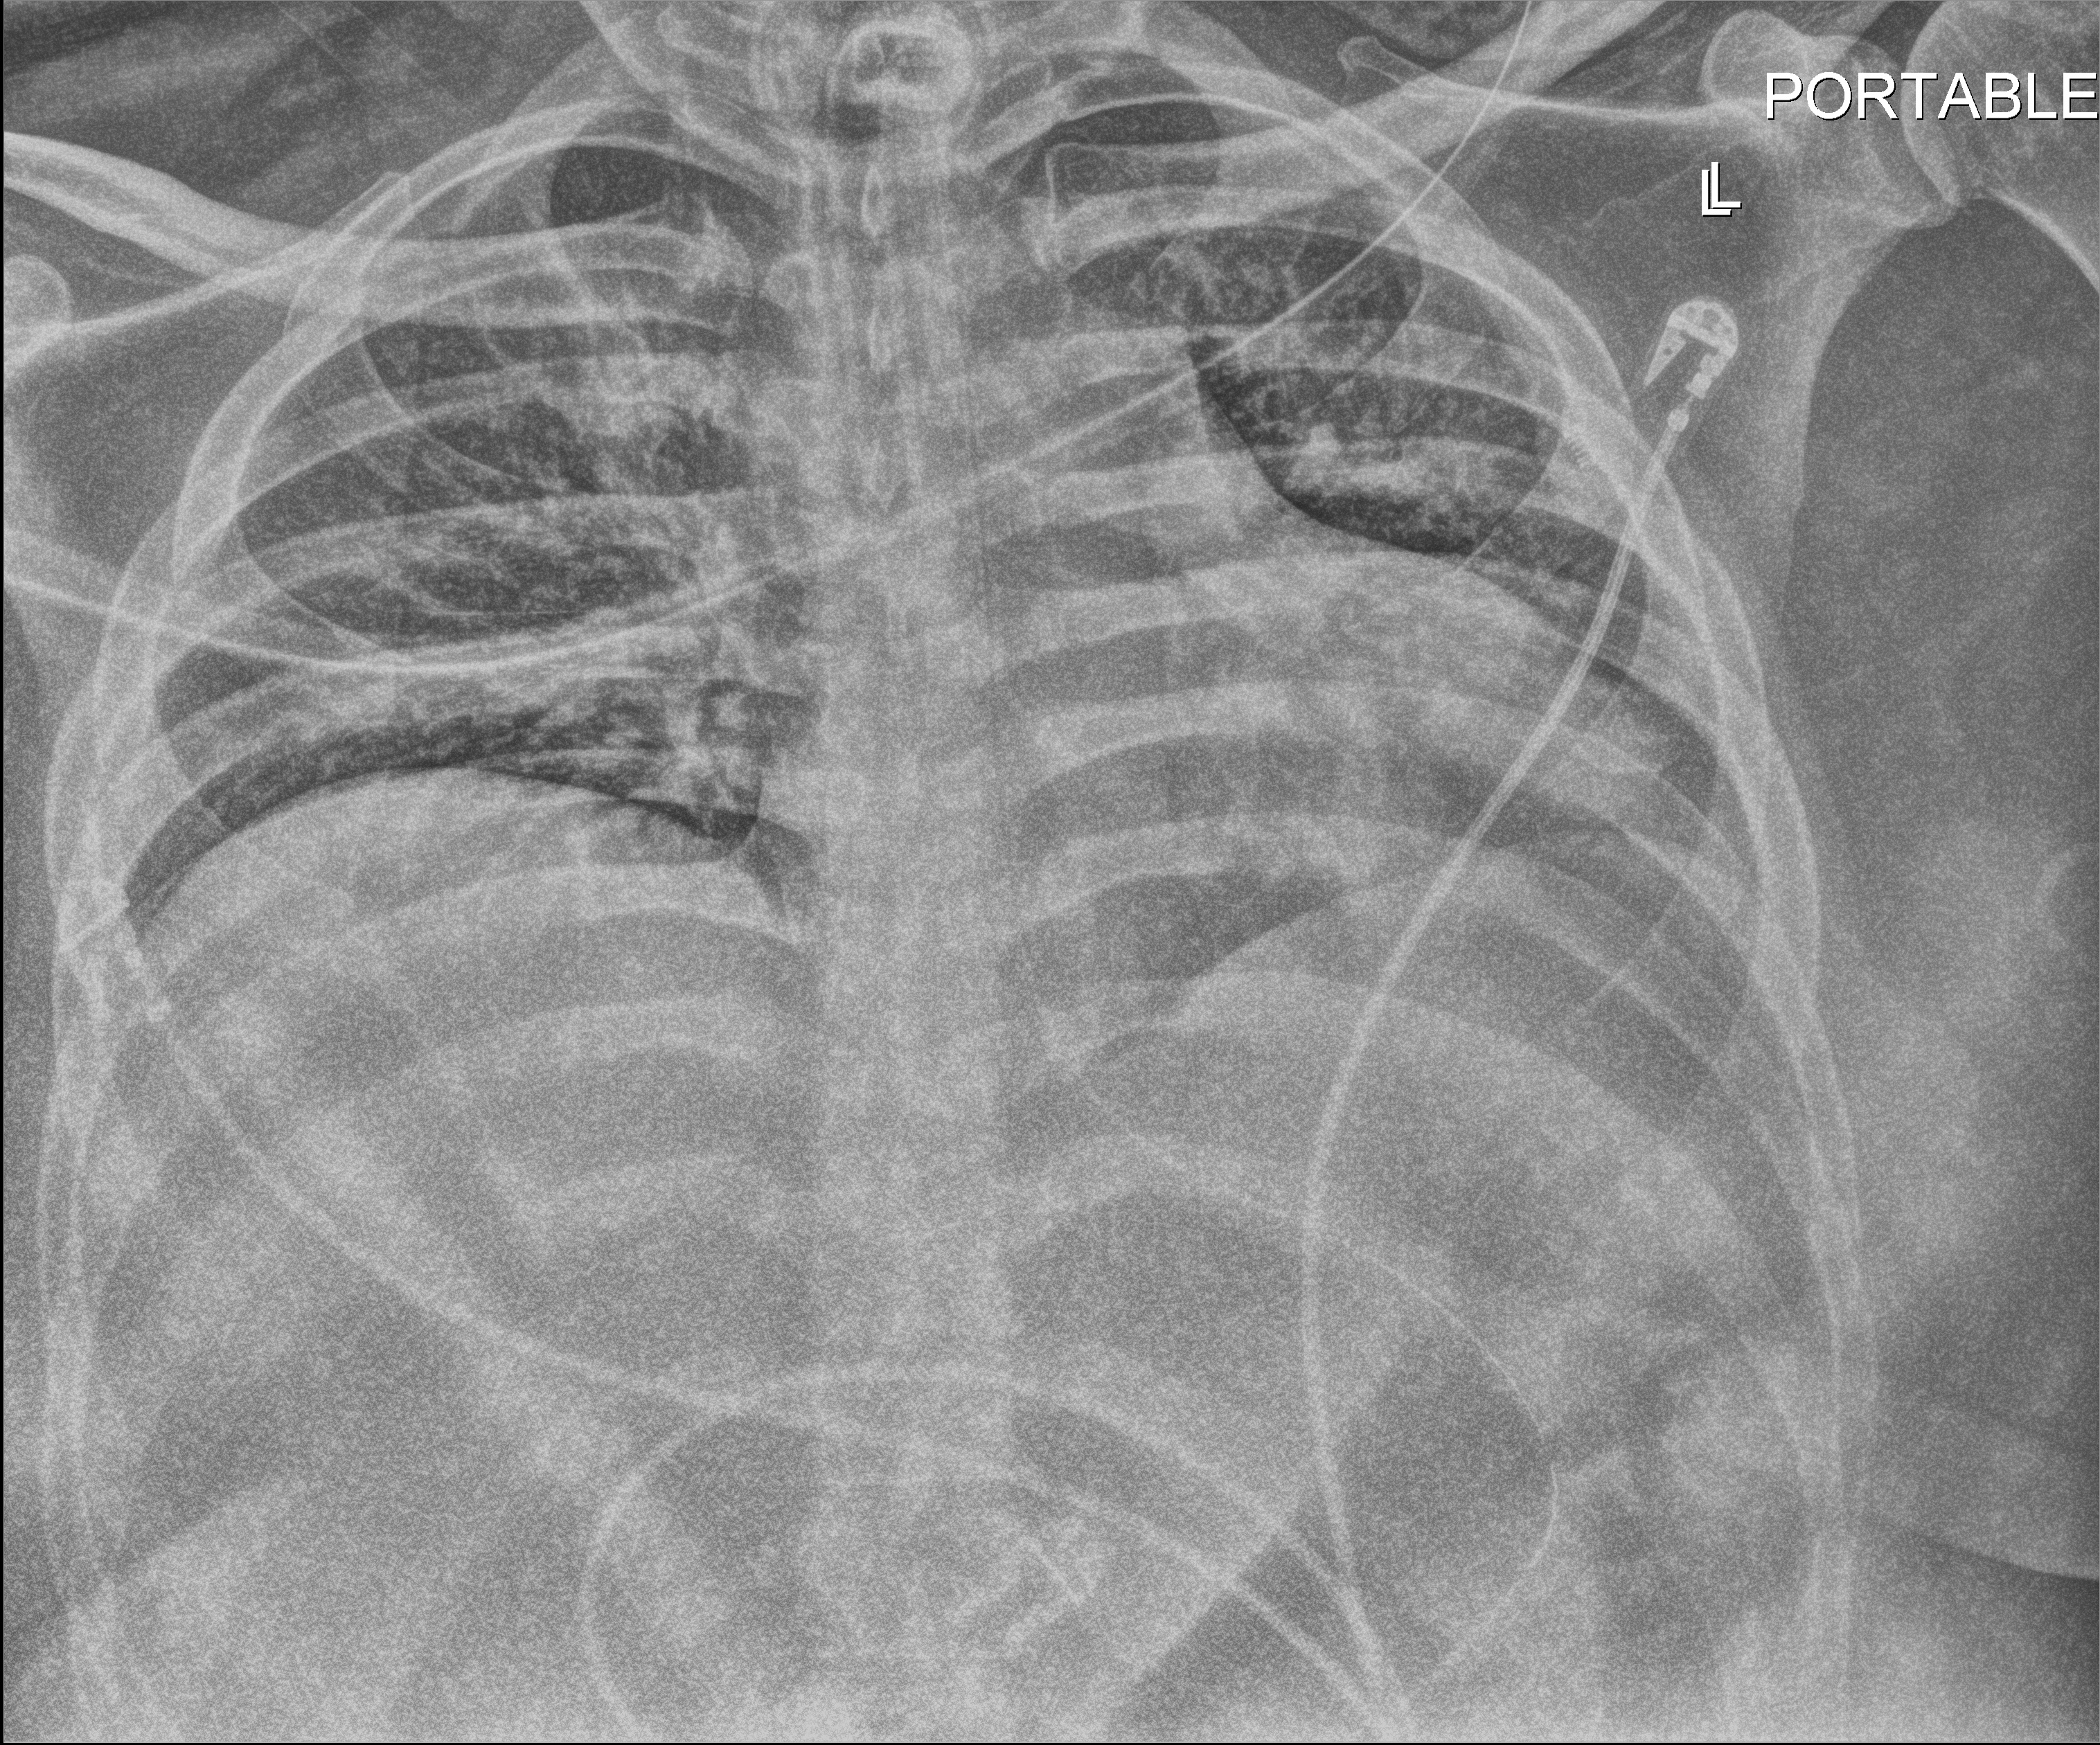
Bedside chest radiograph (digital radiography); anteroposterior (AP) projection. Patient hospitalised with COVID-19; male, aged 18–59 years.
From the hospital-stay record, not from the radiograph (when in the stay this image was taken is not recorded):
- admitted to intensive care during this hospital stay: yes